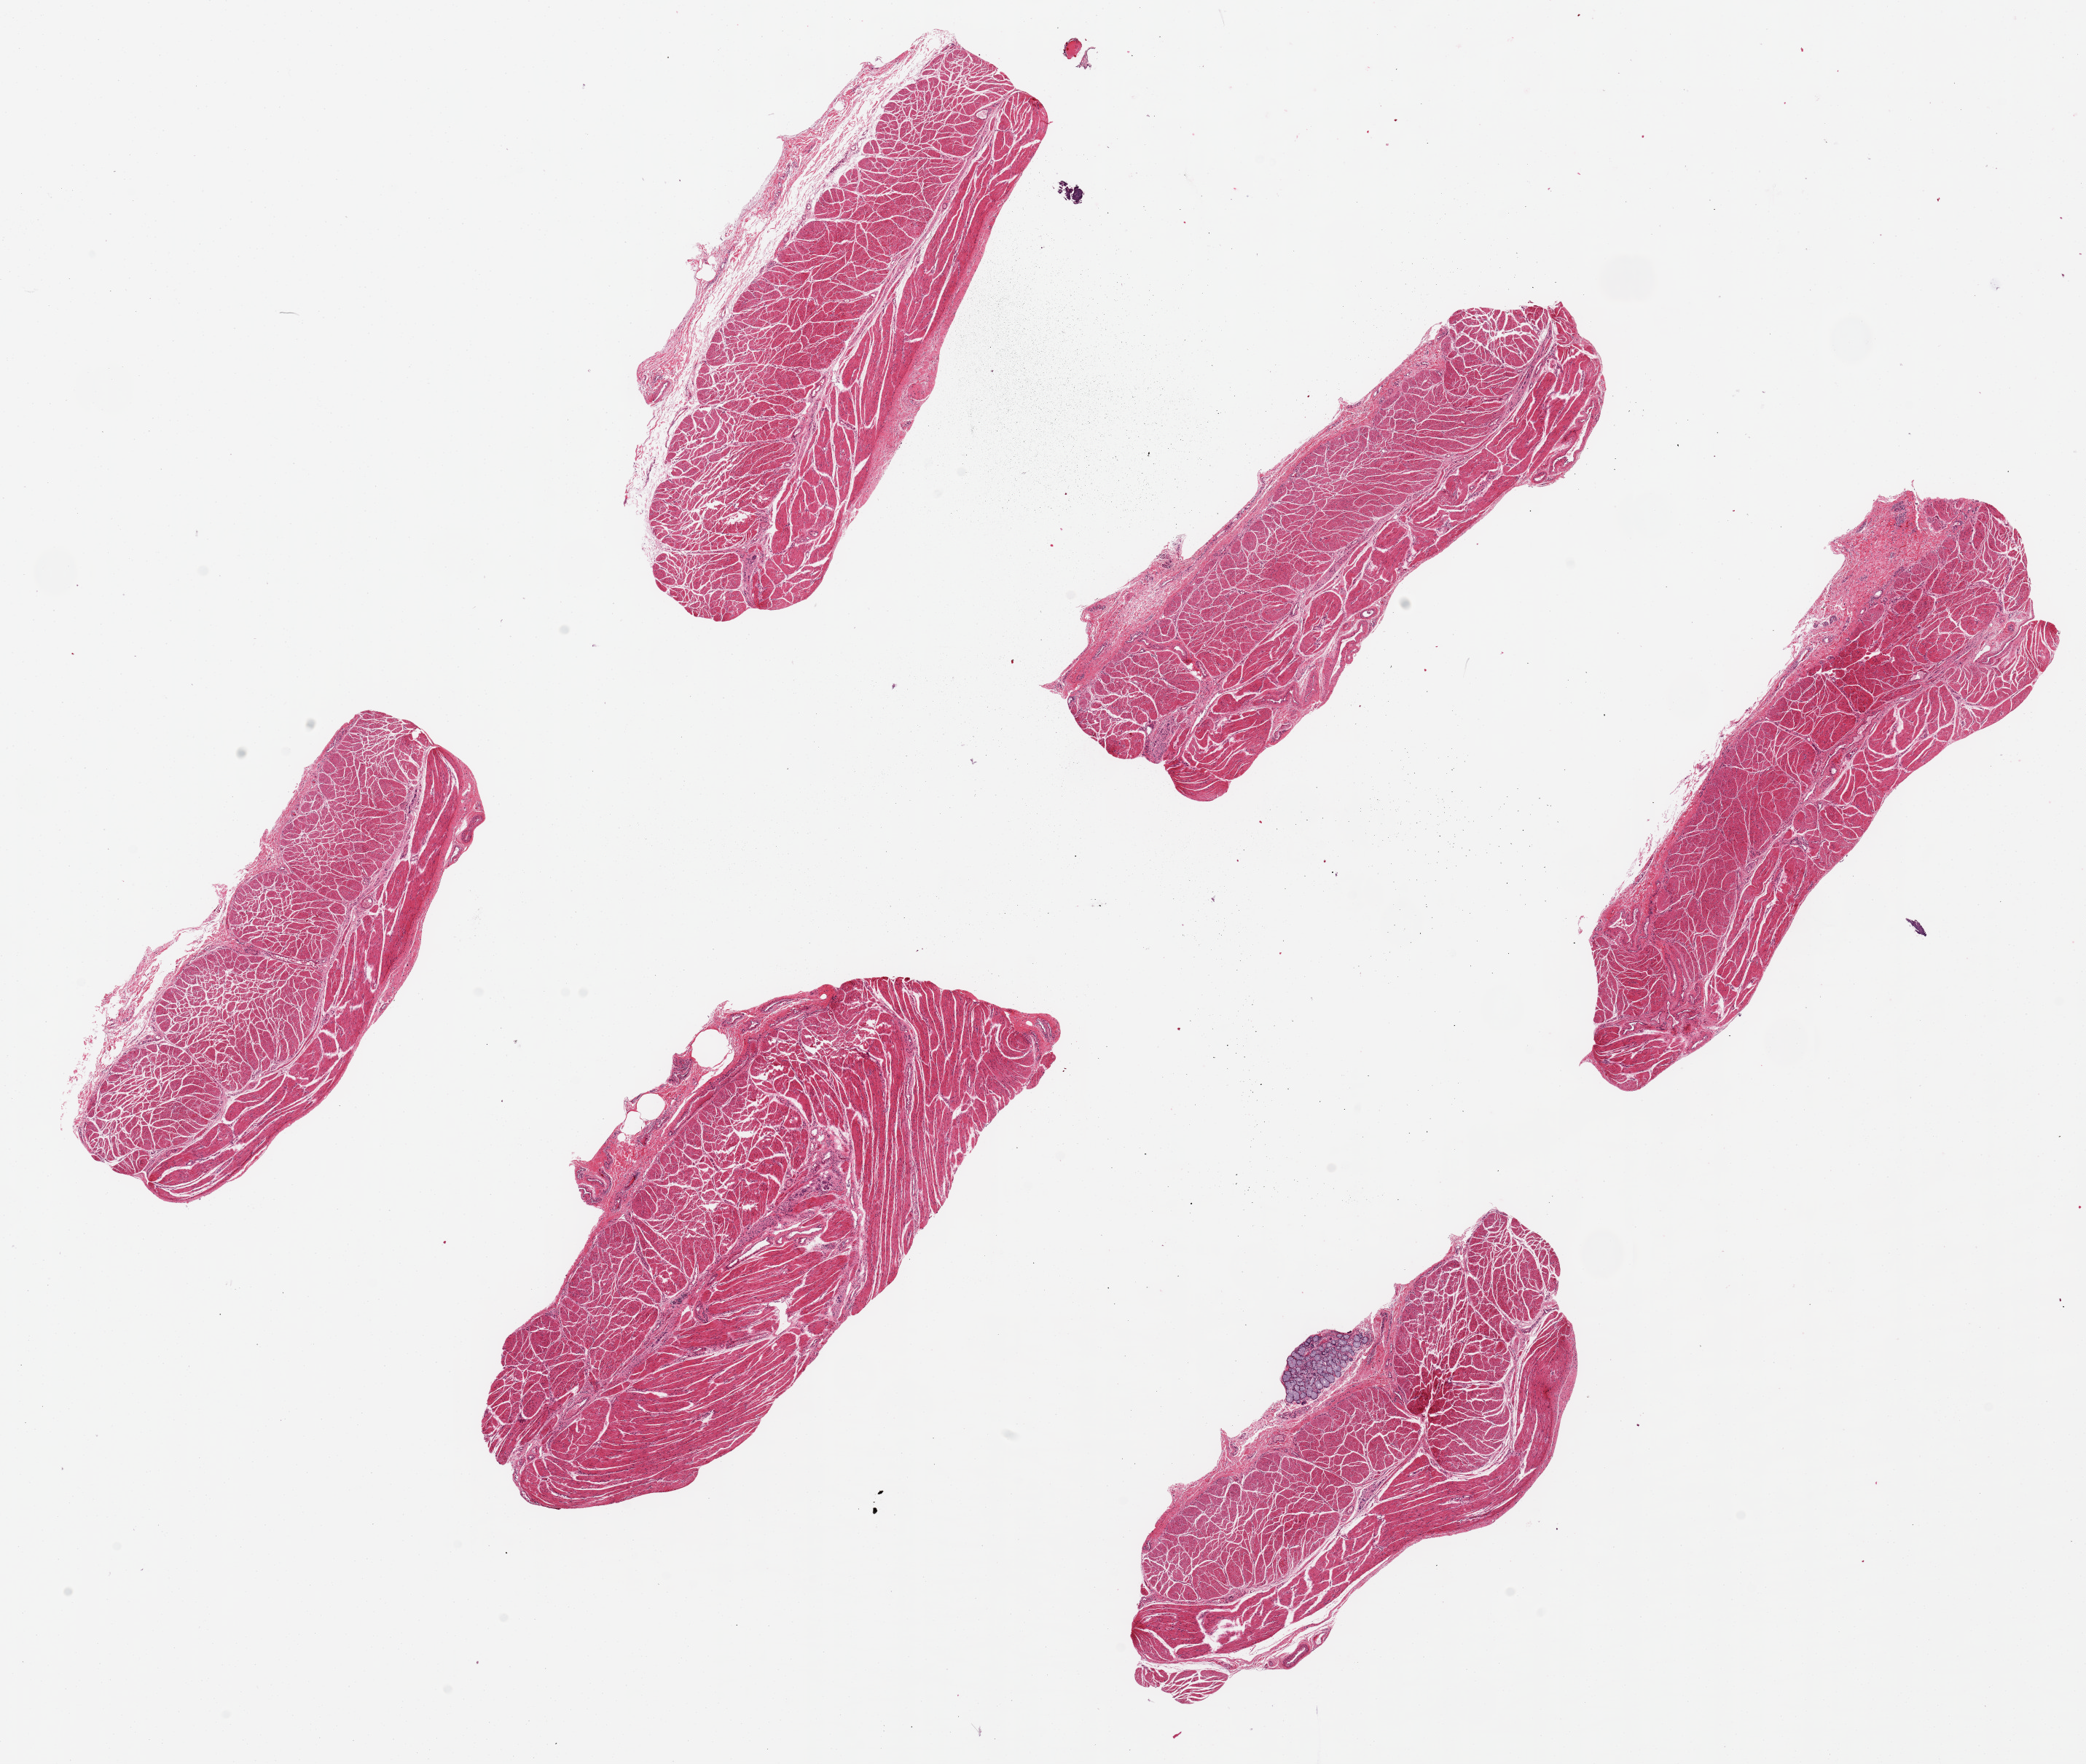
Whole-slide image, haematoxylin and eosin stain, brightfield, whole scanned area (about 22.6 x 19.1 mm) shown as a low-resolution overview; PAXgene-fixed, paraffin-embedded tissue; section of esophageal muscle (target tissue); tissue donor sample. Donor: female.
* pathologist's review note for this sample: 6 ~6.5x2.5mm pieces